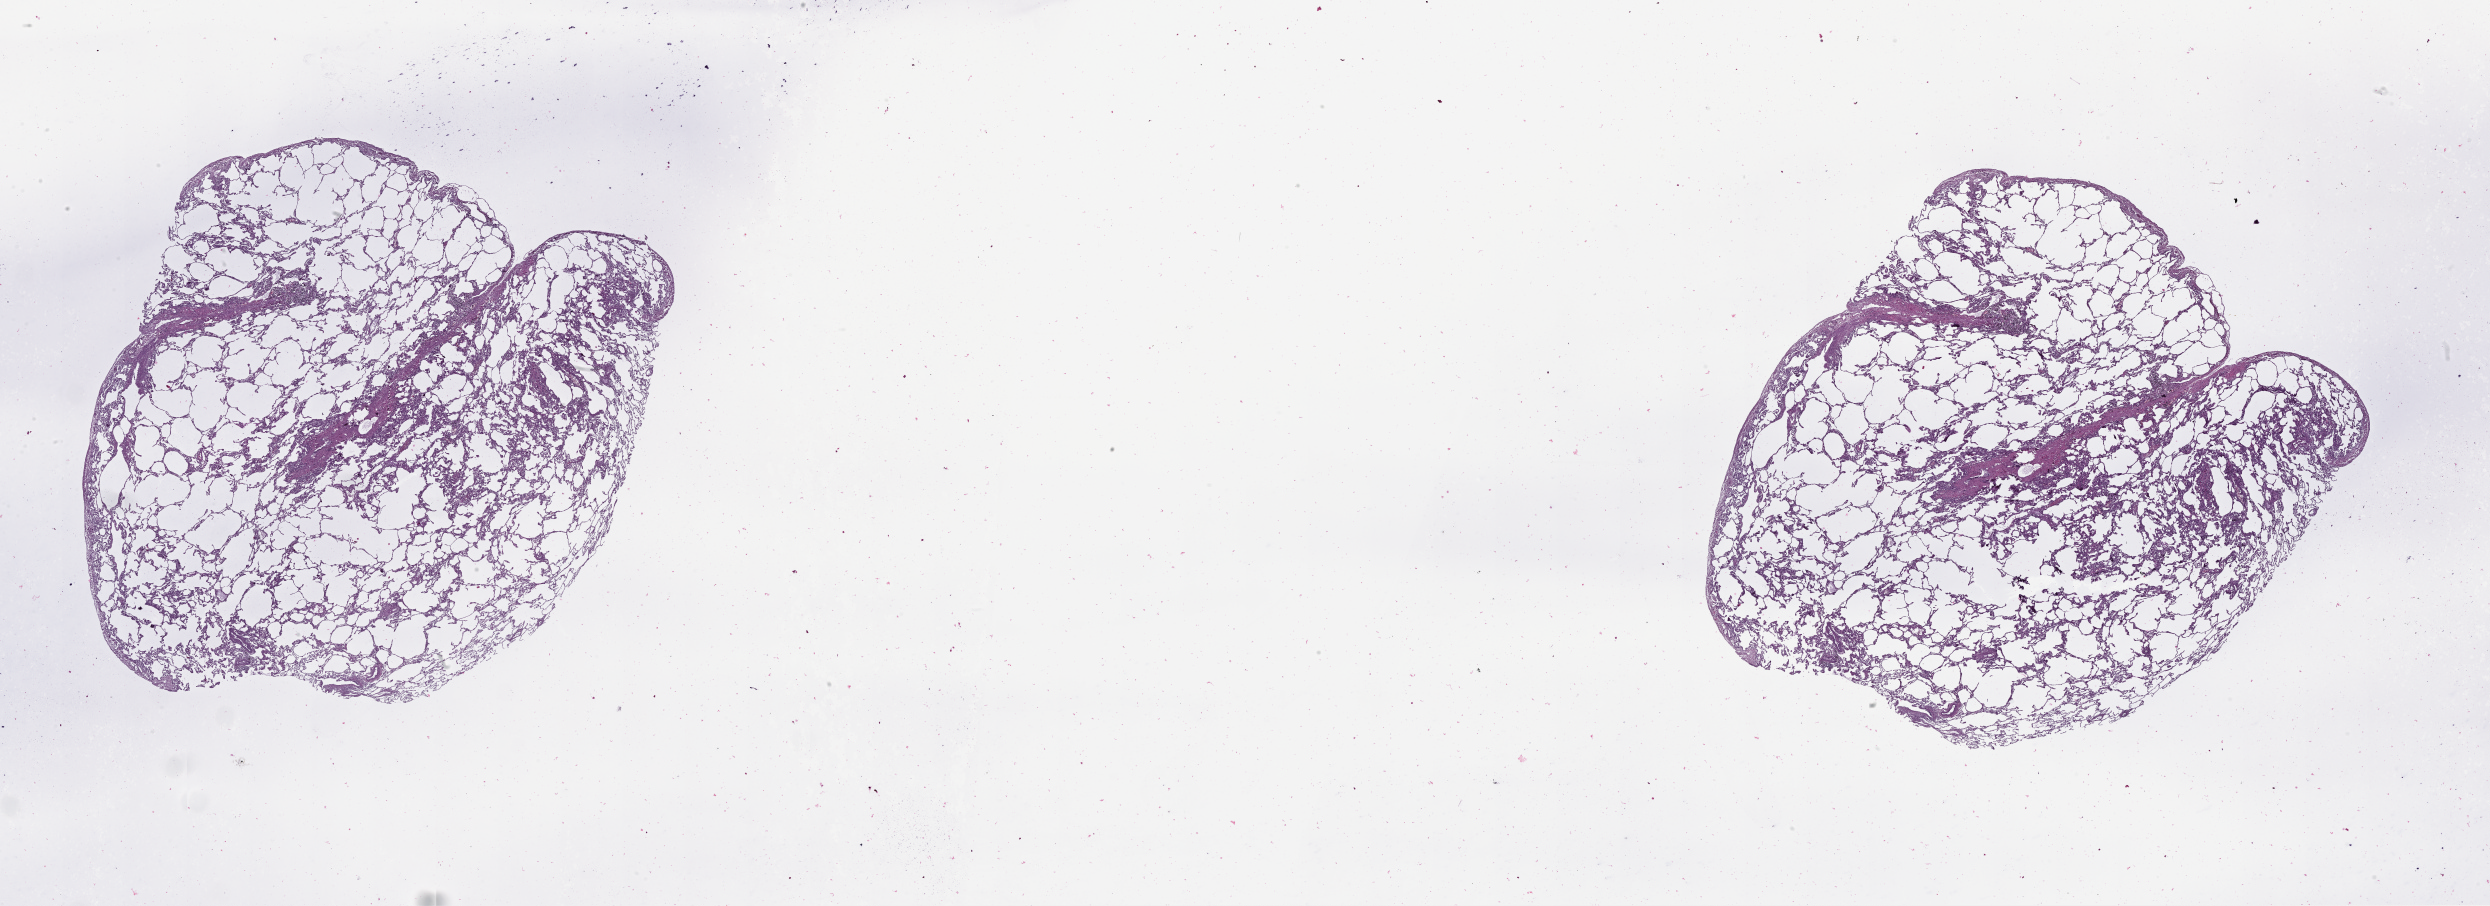
Whole-slide histology image, Hematoxylin and eosin (H&E) stained — low-resolution overview of the scanned area, about 40.1 x 14.6 mm (acquisition: 20x scan). Lung, tissue type not recorded.
• patient diagnosis (cohort enrolment): lung adenocarcinoma (lung)